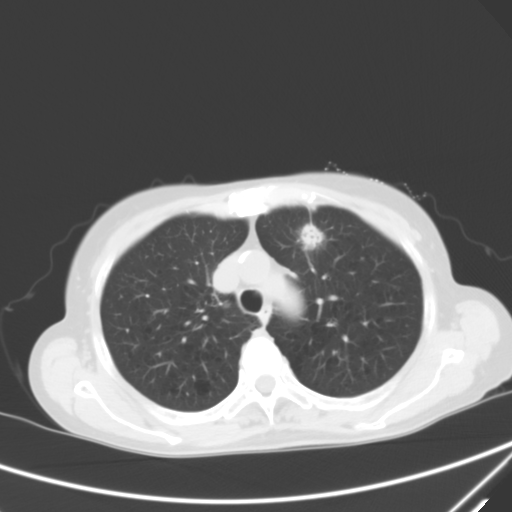
Chest CT, one axial slice. Position 46 of 60 along the scan axis. 120 kVp. Lung window (W 1500 / L -600 HU). 5 mm slice thickness. 512 × 512 image matrix, field of view 350 × 350 mm. Patient: female, 71 years. Case-level facts recorded for this patient, not image findings: clinical TNM (as recorded): T1c N0 M0; histopathological grade: G2-3.
Structures marked on this image (rectangle marked by the reading radiologist):
- lung tumour (recorded histology: adenocarcinoma): bounding box [x1, y1, x2, y2] px = [290, 217, 325, 255]